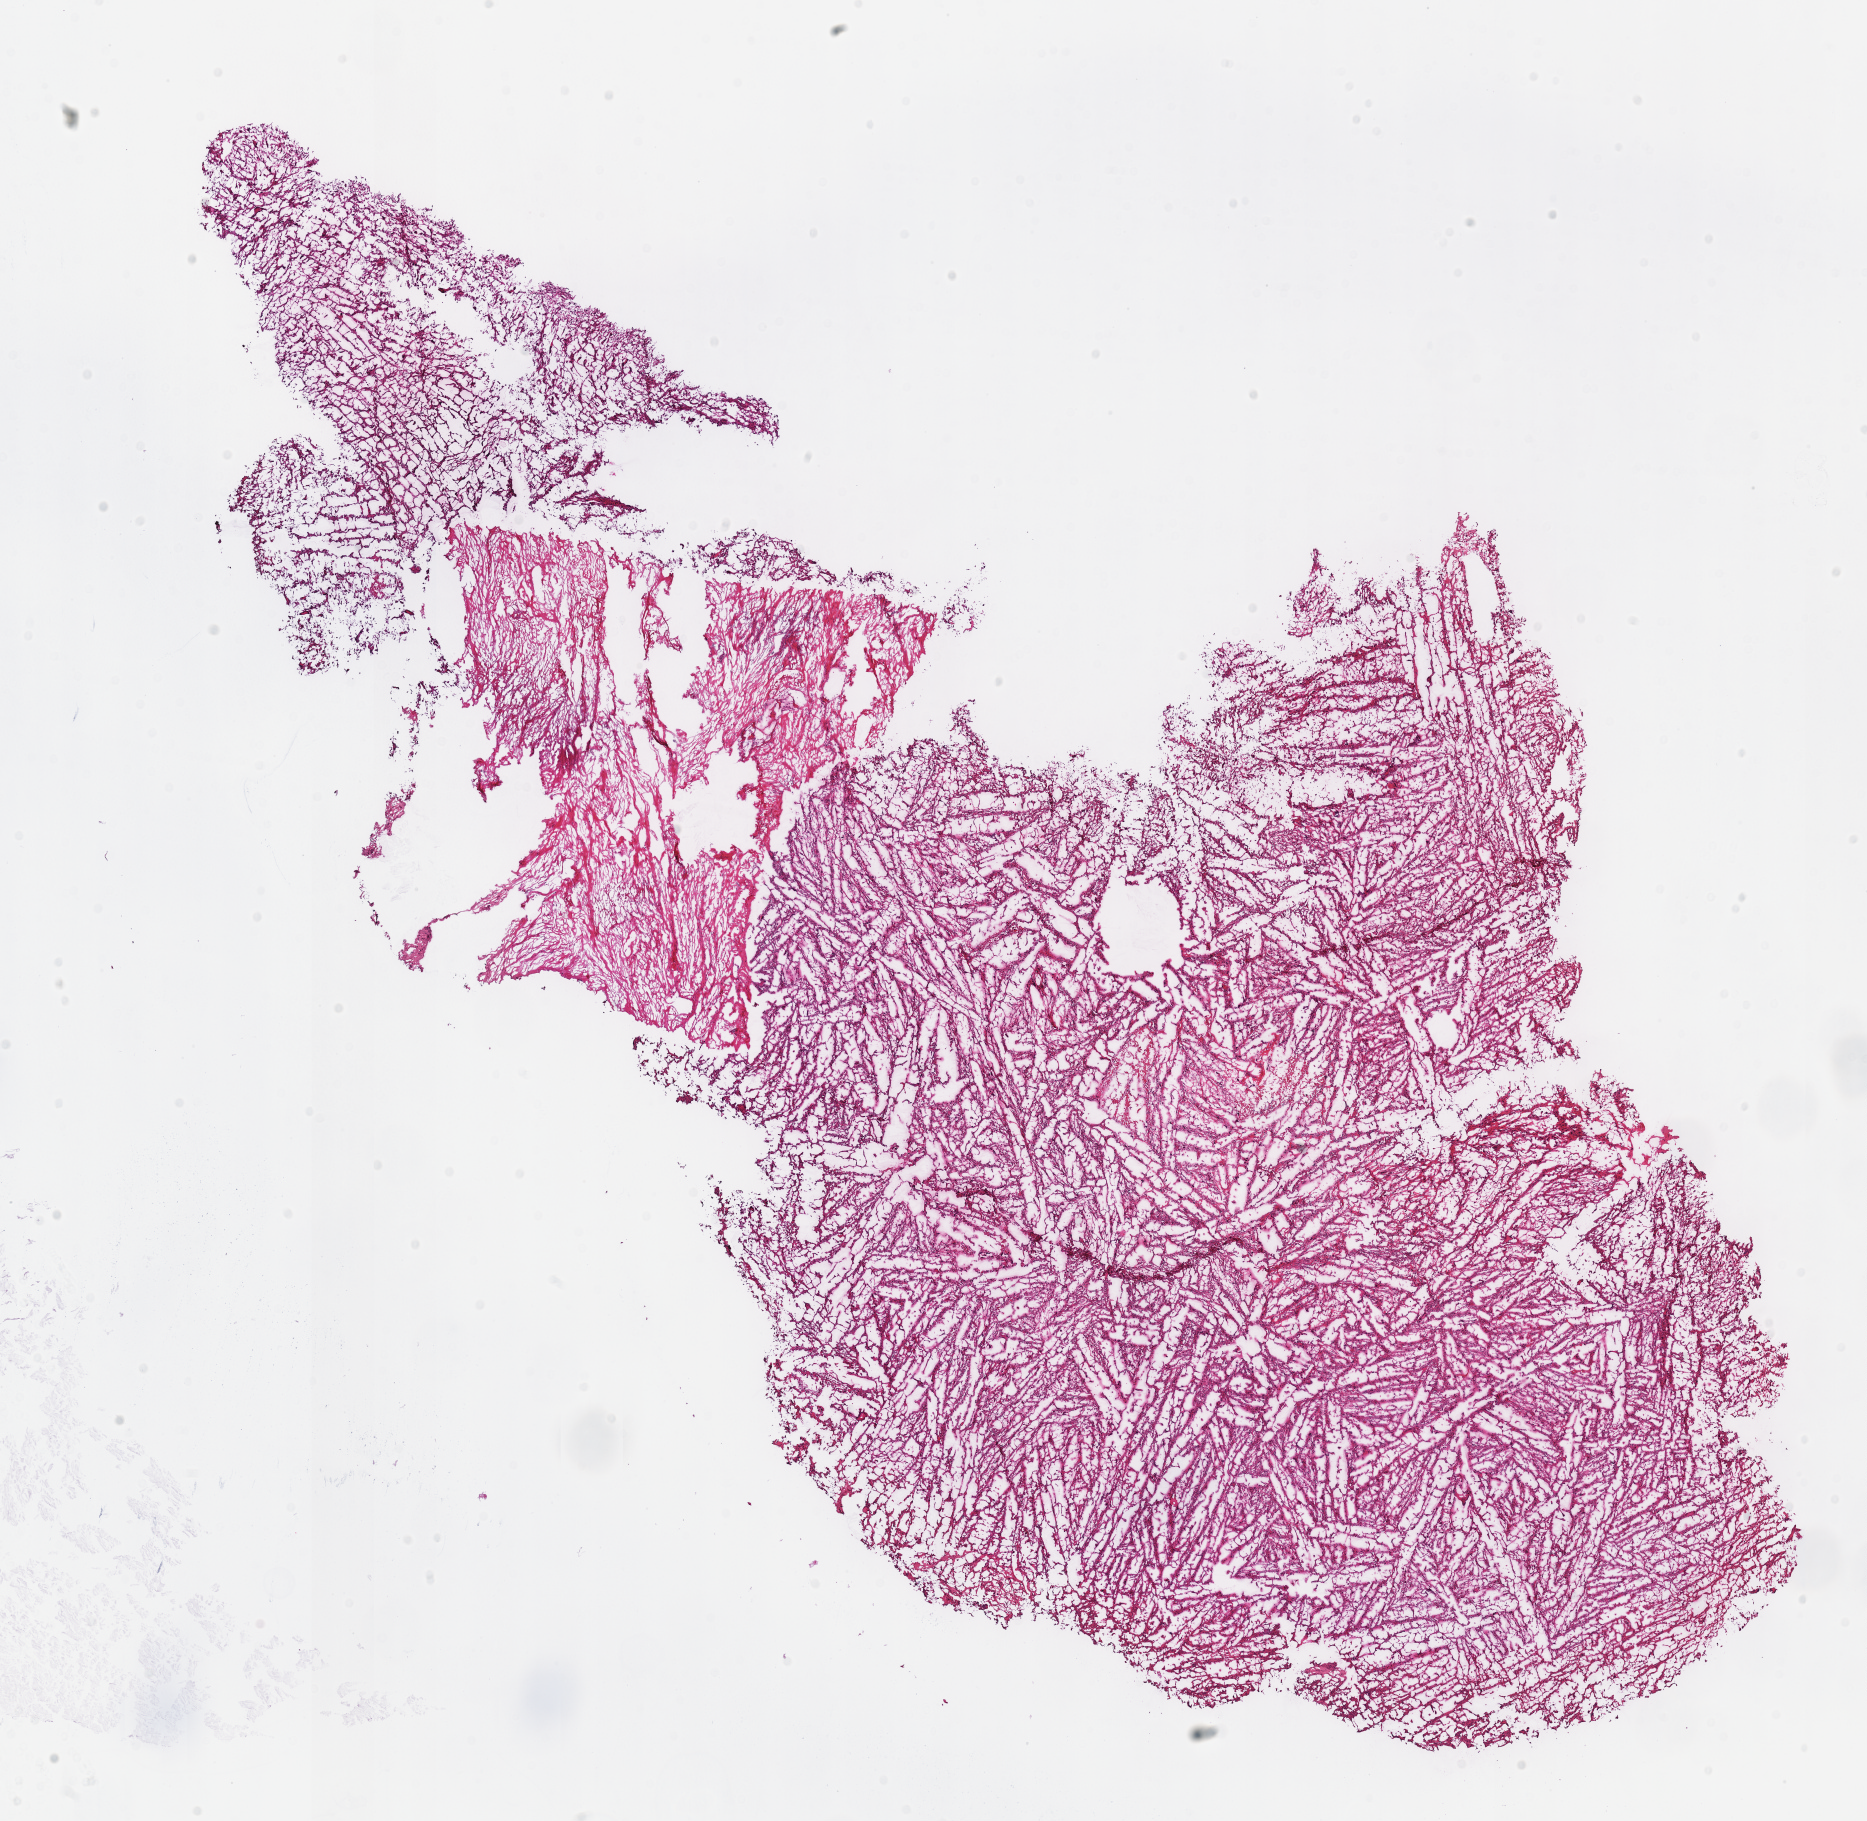
Whole-slide histology image, H&E-stained — whole scanned area (about 14.7 x 14.3 mm) shown as a low-resolution overview, frozen section, primary tumour sample from the kidney. Patient: male, age at initial diagnosis 78 years. Composition of this section per pathologist review: tumour cells 85%, tumour nuclei 85%, normal cells 0%, stromal cells 15%, necrosis 0%.
• laterality: right
• AJCC pathologic stage: IV
• histologic diagnosis: Renal cell carcinoma, chromophobe type
• TNM: T4 NX